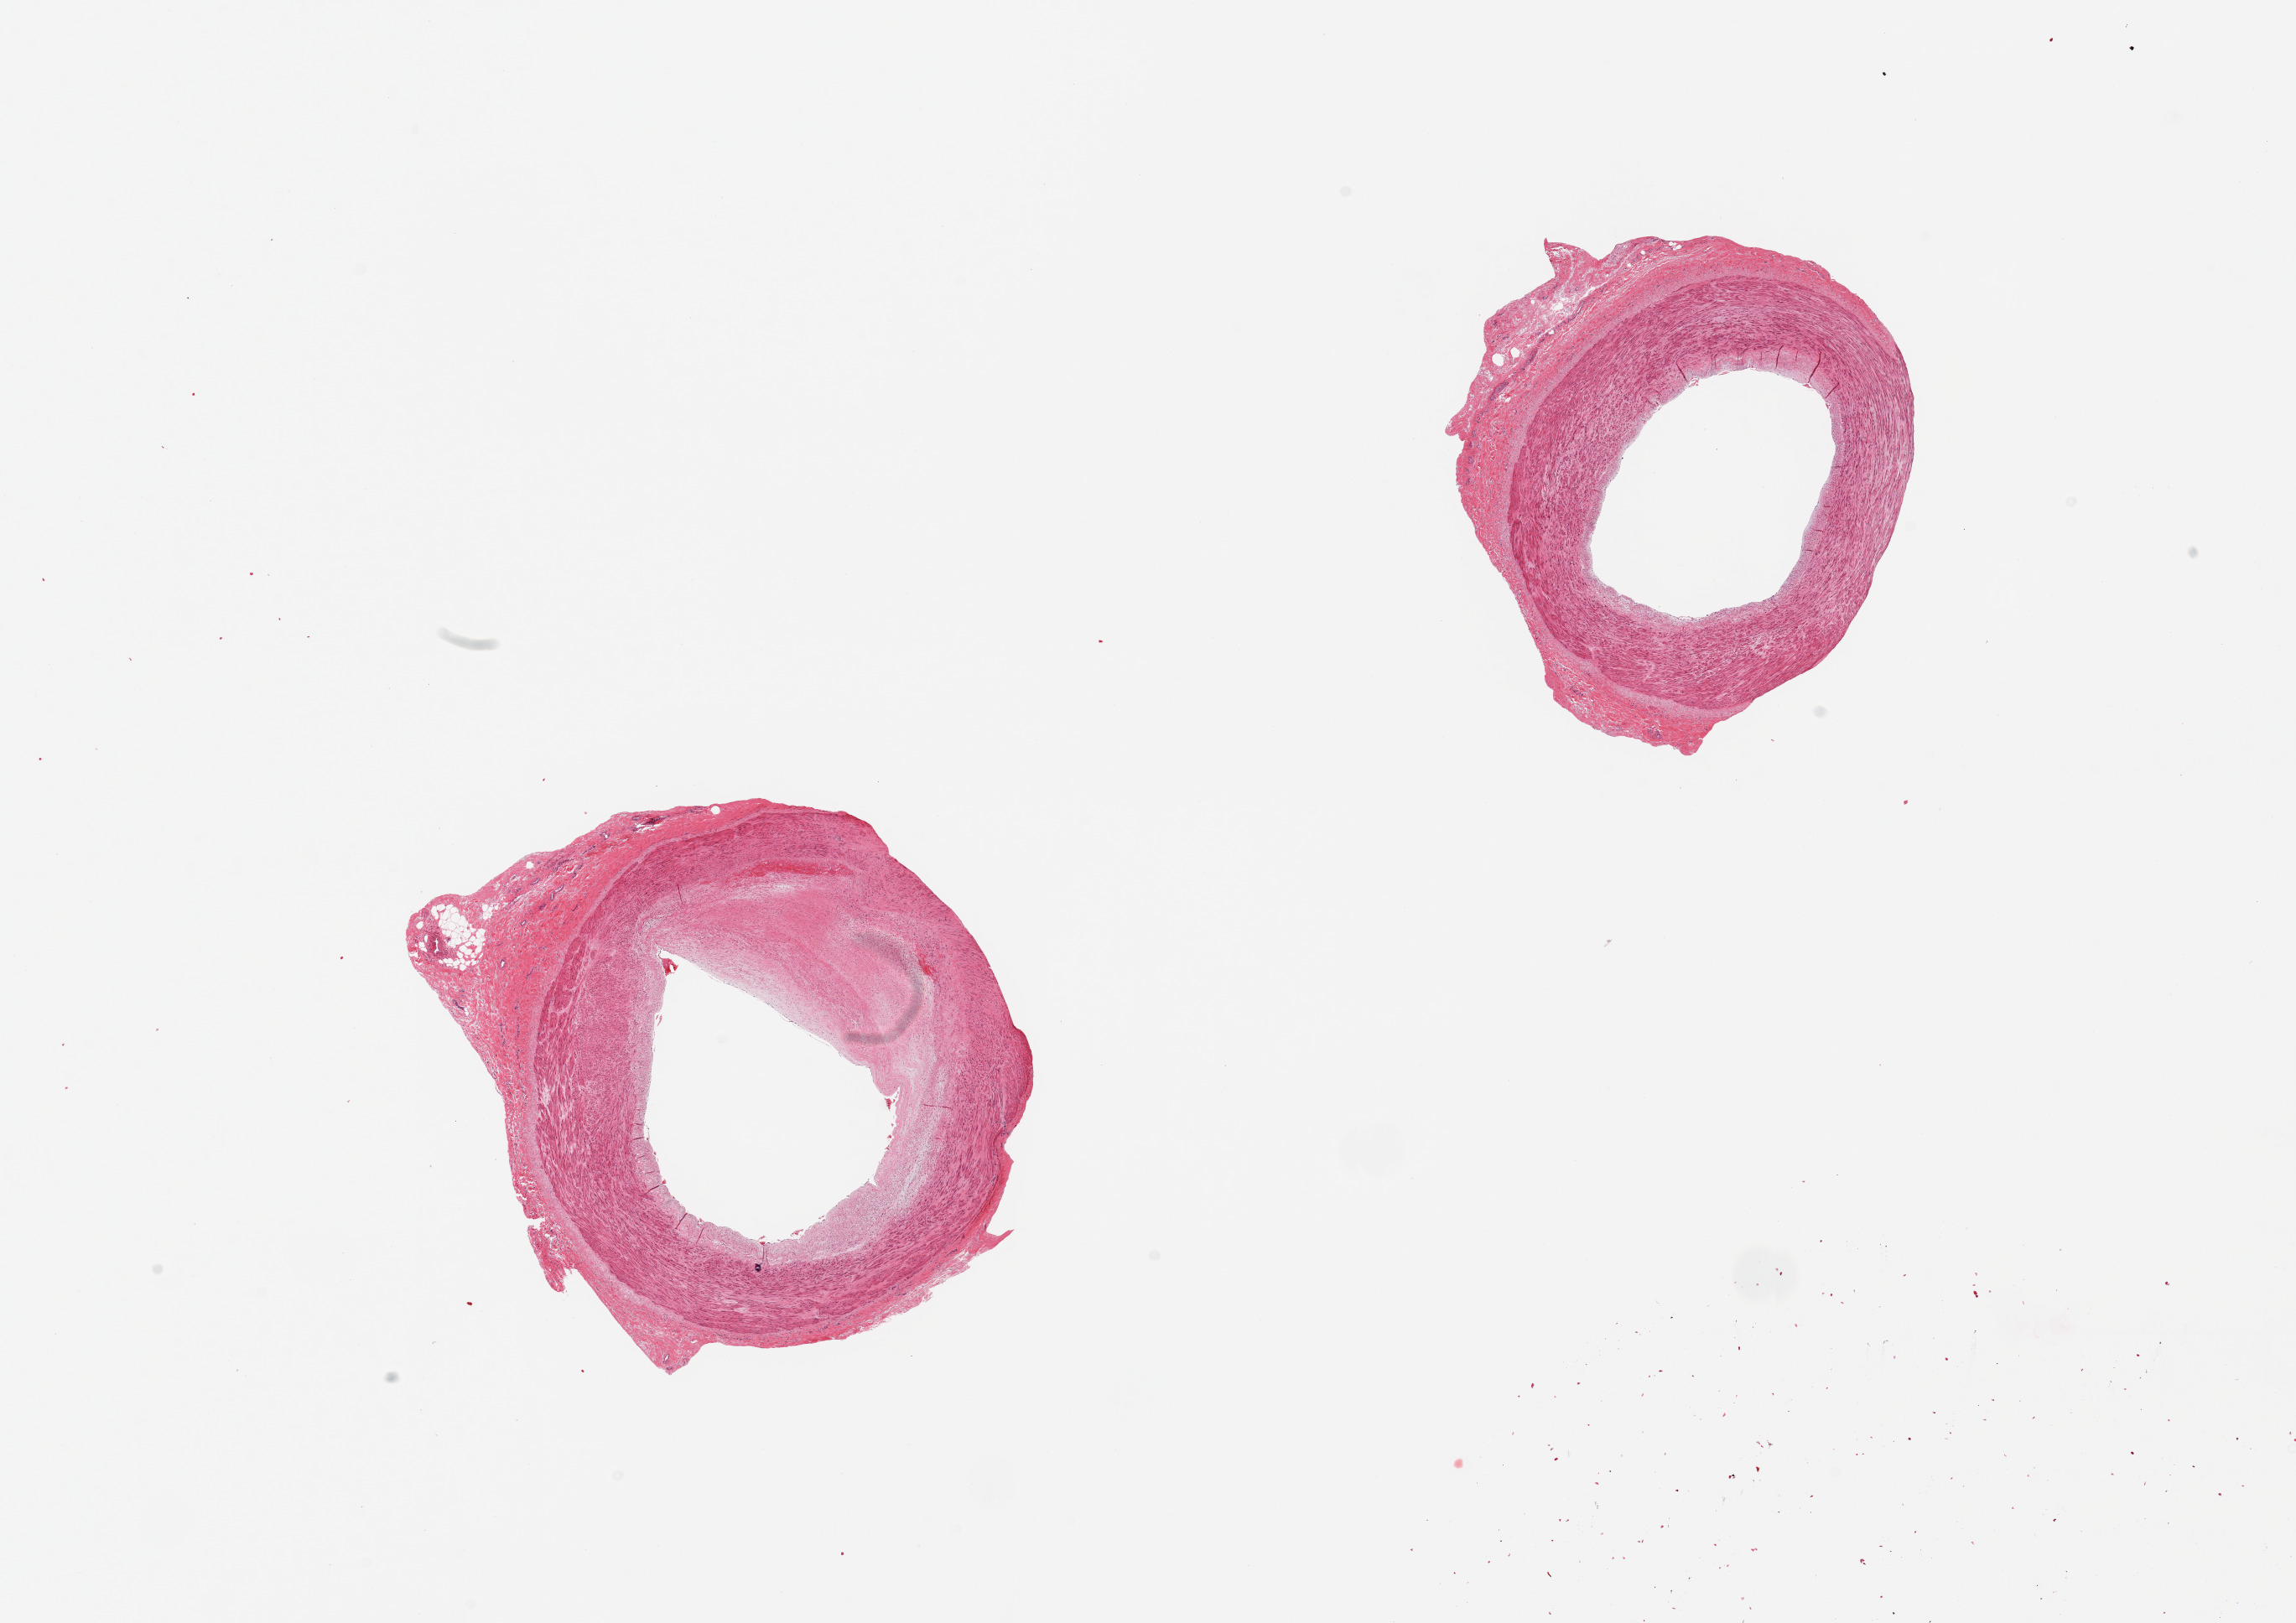
Whole-slide image, hematoxylin and eosin (H&E) stain, brightfield, a low-resolution overview of the entire scanned area, about 21.7 x 15.3 mm; PAXgene-fixed paraffin-embedded (PFPE) section; sampled site (target tissue): tibial artery; donor tissue sample. Donor sex: male.
Reviewer comment on this tissue sample: 2 pieces, clean specimens, one with ~50% occlusion by atherosis.